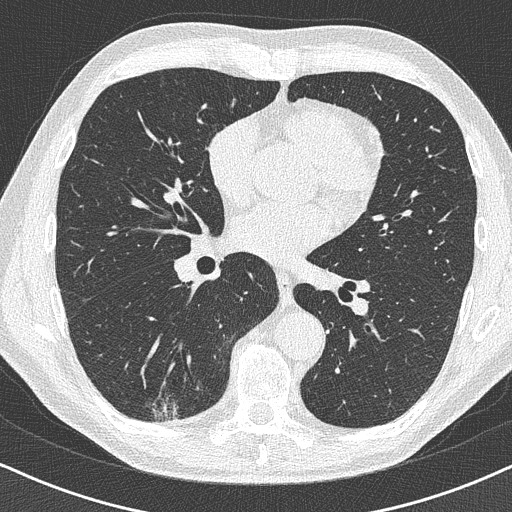
Low-dose screening chest CT, axial slice, baseline screening round, lung window (W 1500 / L -600 HU), 1 mm slice thickness, lung (sharp) reconstruction kernel (B50f), 120 kVp, slice 226 of 438 in the series. Male, age 63 years at enrolment.
- Expert reader's lesion annotation, bounding box (x1, y1, x2, y2) in pixels: (127, 358, 199, 428).
- Screening reader's record for this exam (one nodule recorded; not confirmed to be the boxed lesion): non-calcified nodule or mass ≥4 mm, right lower lobe, 16 × 13 mm, poorly defined margins.
- Official screen result: positive, change unspecified: nodule(s) >= 4 mm or enlarging nodule(s), mass(es), or other non-specific abnormalities suspicious for lung cancer.
- Participant outcome: lung cancer diagnosed 74 days after this screen — adenocarcinoma, NOS, right lower lobe, moderately differentiated (G2), stage IA (AJCC 6th edition), 20 mm at pathology.